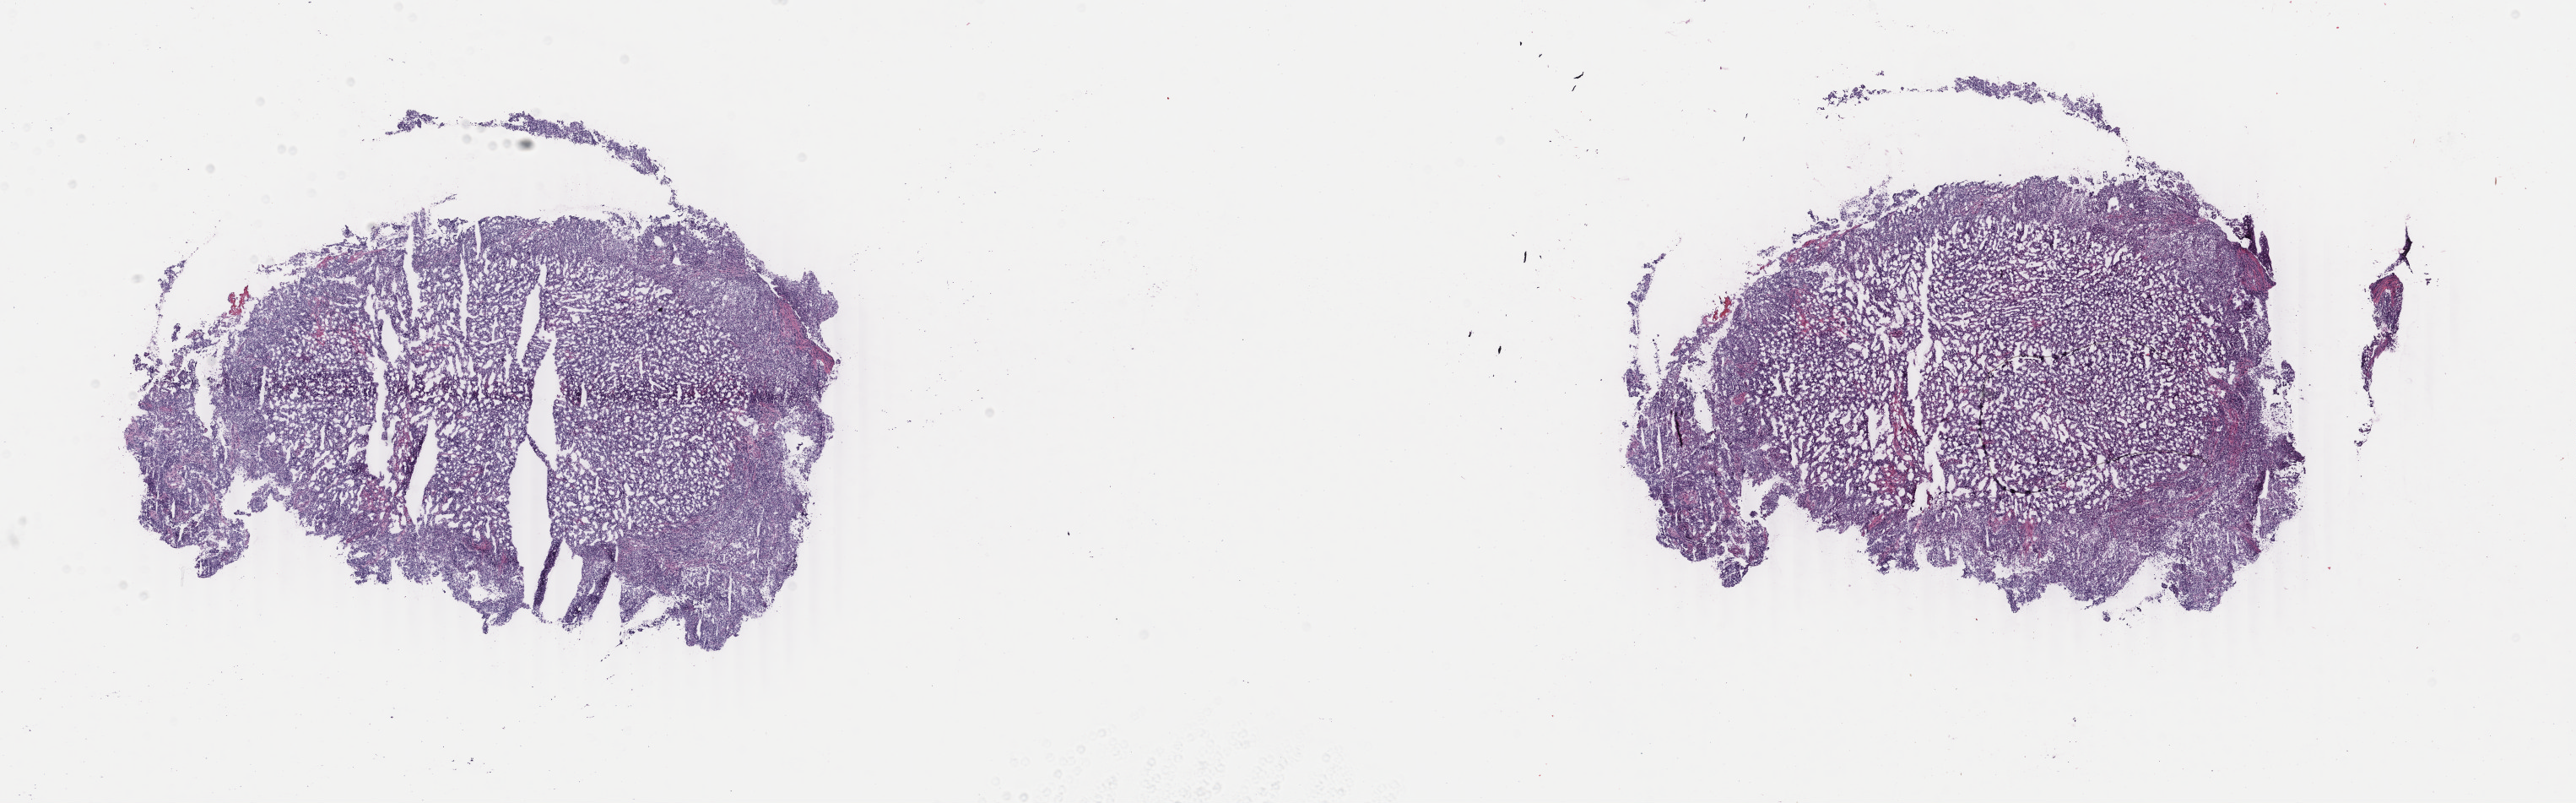
Digitized Hematoxylin and eosin (H&E) stained tissue section (whole slide) — shown as a low-resolution overview of the whole scanned area (about 24.3 x 7.6 mm), frozen section from the top of the tissue portion, primary tumour sample from the uterus. Female, age 58 years at initial diagnosis. Histologic grade: G3 (poorly differentiated). Pathologist review of this section (percent, as recorded): tumour cells 85%, tumour nuclei 85%, normal cells 0%, stromal cells 10%, necrosis 5%. Infiltration values recorded for this section: lymphocyte infiltration 50%, monocyte infiltration 30%, neutrophil infiltration 40%.
FIGO stage: IVB. Diagnosis: Endometrioid adenocarcinoma, NOS (endometrium).